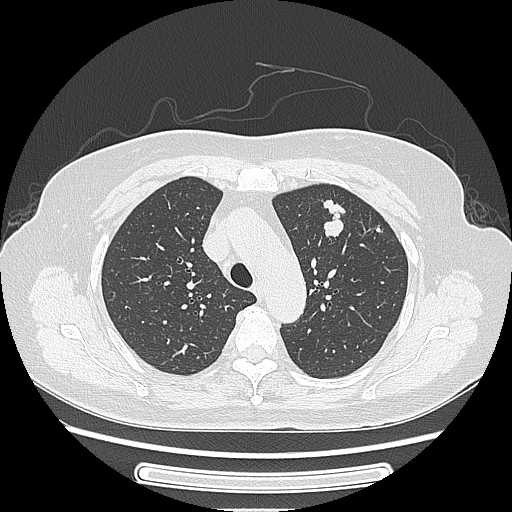
Chest CT, one axial slice; slice 176 of 227 in the series (ordered by position); 120 kVp; lung window (W 1500 / L -600 HU); 1.25 mm slice thickness; 512 × 512 image matrix. Patient: female, 77 years. Case-level facts recorded for this patient, not image findings: clinical TNM (as recorded): T1c N3 M0.
Annotated regions visible in this slice (rectangle marked by the reading radiologist):
- lung tumour (recorded histology: adenocarcinoma): bounding box (x1, y1, x2, y2) in pixels: (314, 189, 354, 237)